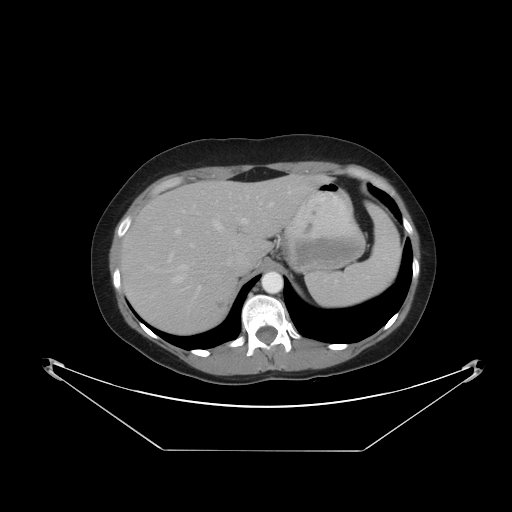
Contrast-enhanced abdominal CT, one axial slice; slice 34 of 48 in the series (ordered by position); 120 kVp; intravenous contrast given; soft-tissue window (W 400 / L 40 HU); 512 × 512 image matrix. Female patient, age 38 years. Case-level facts recorded for this patient, not image findings: diagnosis: colorectal cancer liver metastases, imaged before liver resection; multiple liver metastases: yes; largest metastasis: 2.5 cm.
Structures marked on this image (outlined manually by an expert reader):
- hepatic veins: bounding box [x1, y1, x2, y2] px = [173, 194, 261, 283]
- liver: [120, 176, 326, 336]
- planned liver remnant (the part of the liver to remain after resection): [185, 177, 309, 256]
- portal vein (with intrahepatic branches): [176, 191, 291, 289]
- liver metastasis: [213, 299, 229, 310]
- liver metastasis: [307, 177, 319, 190]